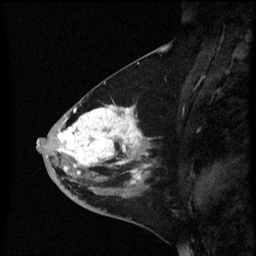
Breast MRI (dynamic contrast-enhanced), one sagittal slice; slice 27 of 60 in the series (ordered by position); dynamic contrast-enhanced series, image 2 of 3 at this slice position (ordered by acquisition); 1.5 T; TE 4.2 ms, TR 8.4 ms; 256 × 256 image matrix. Female patient, age 46 years. Case-level facts recorded for this patient, not image findings: setting: breast cancer imaged before/during neoadjuvant chemotherapy; receptor status: HER2-positive.
Outlined on this slice (semi-automatic segmentation, software-assisted and operator-edited):
- analysis volume of interest (the breast-tissue region the enhancement analysis was run in; not a lesion): bounding box (x1, y1, x2, y2) in pixels: (37, 96, 156, 187)
- tumour enhancement mask (voxels above the 70 % enhancement threshold inside the analysis volume of interest): (58, 106, 142, 185)